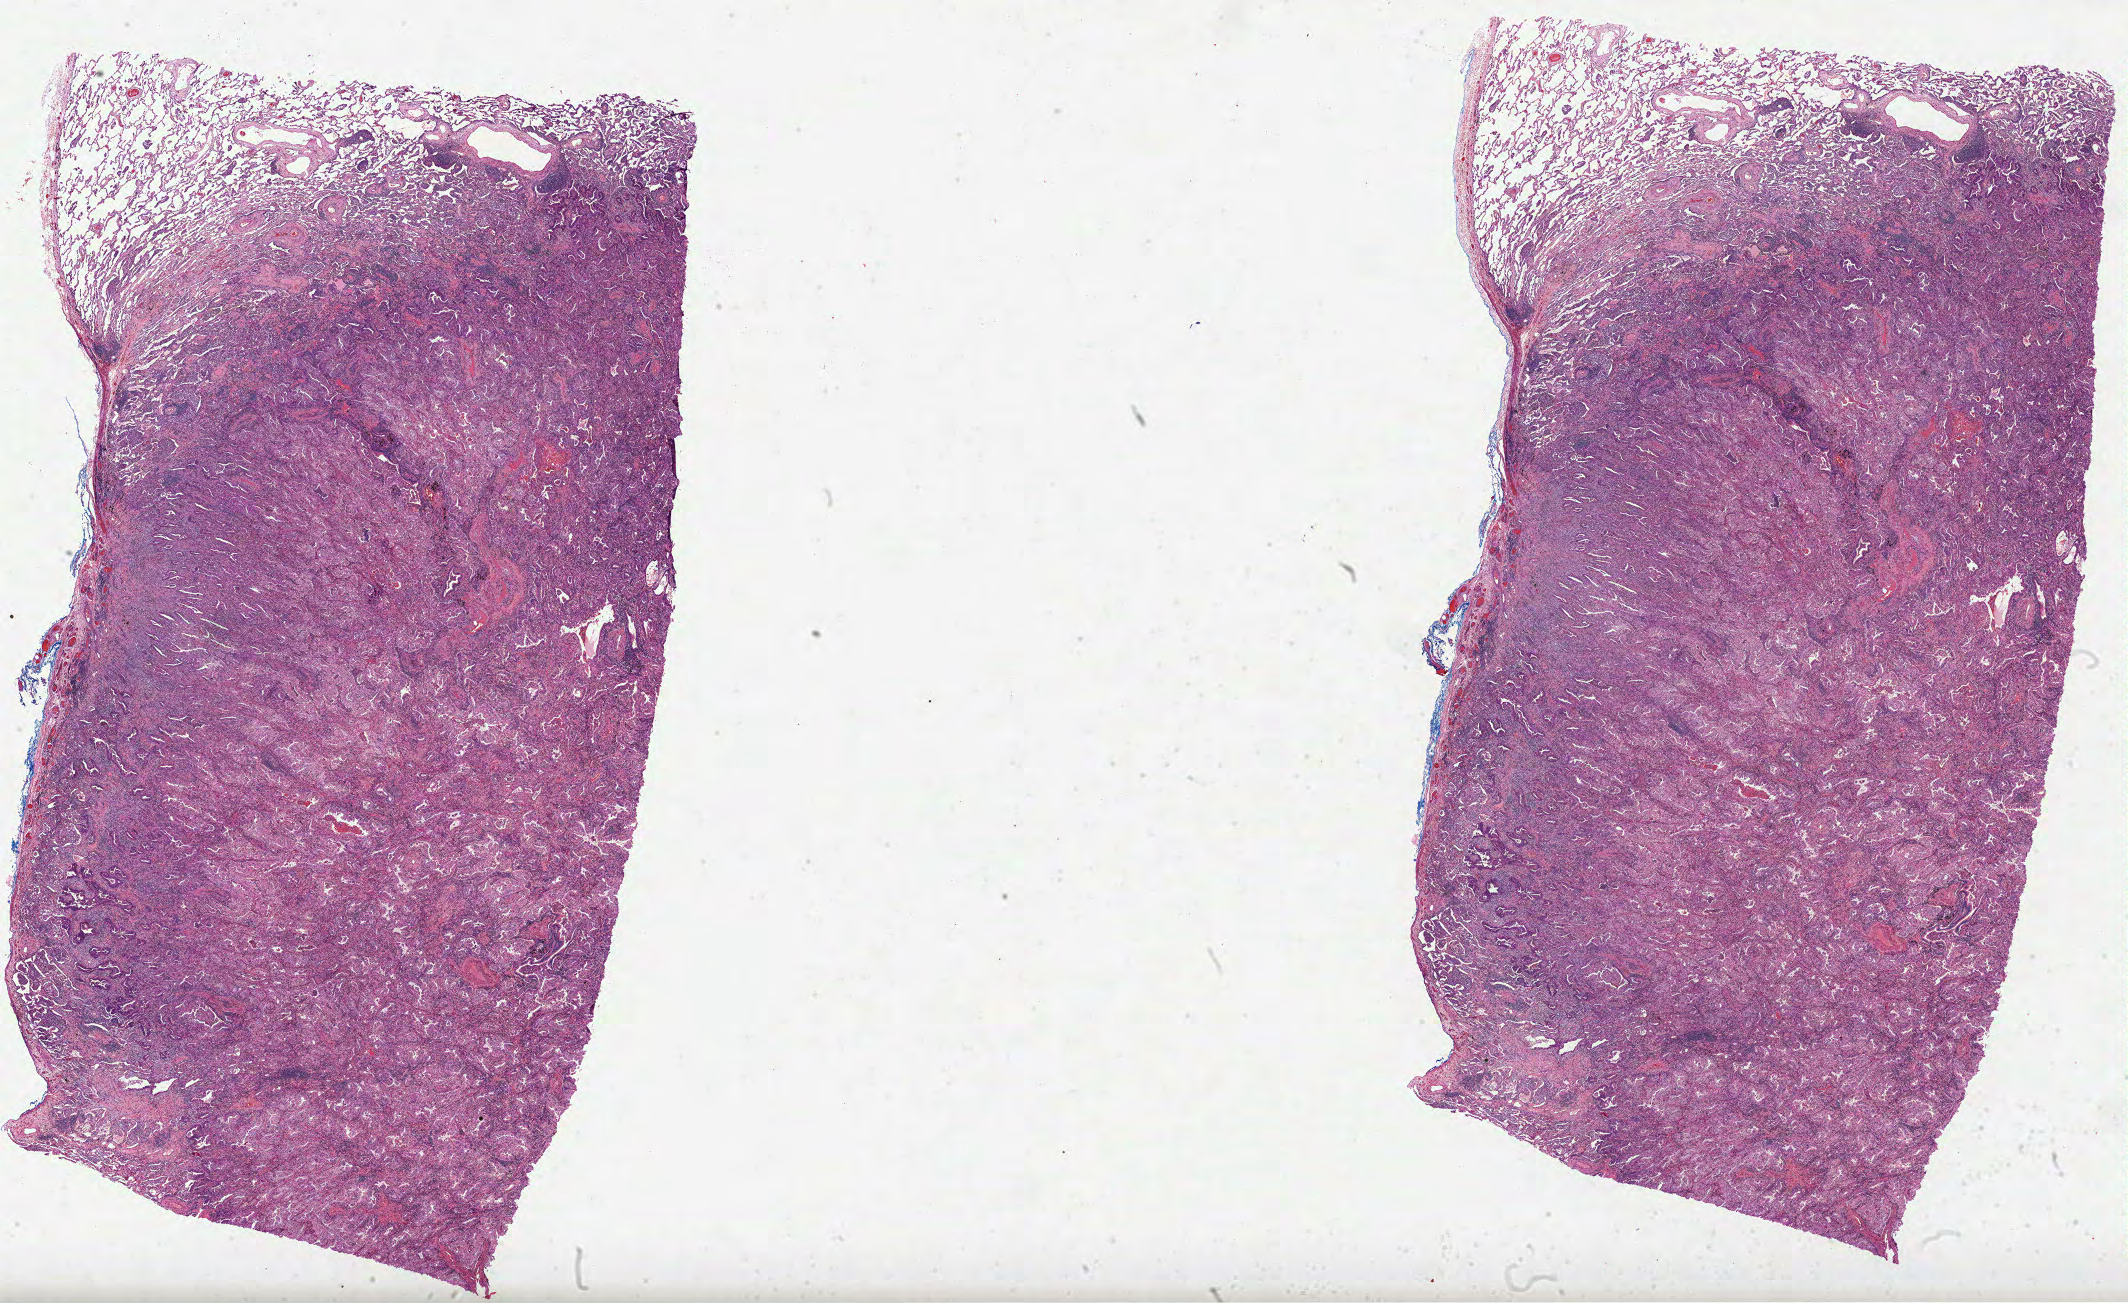
Hematoxylin and eosin (H&E) stained whole-slide image — shown as a low-resolution overview of the whole scanned area (about 34.3 x 21.0 mm). Formalin-fixed paraffin-embedded (FFPE) diagnostic section. Lung, primary tumour sample. Male patient; age at initial diagnosis 84 years.
Pathologic diagnosis: Acinar cell carcinoma (lower lobe, lung). Laterality: left. AJCC pathologic stage: IB (7th edition).